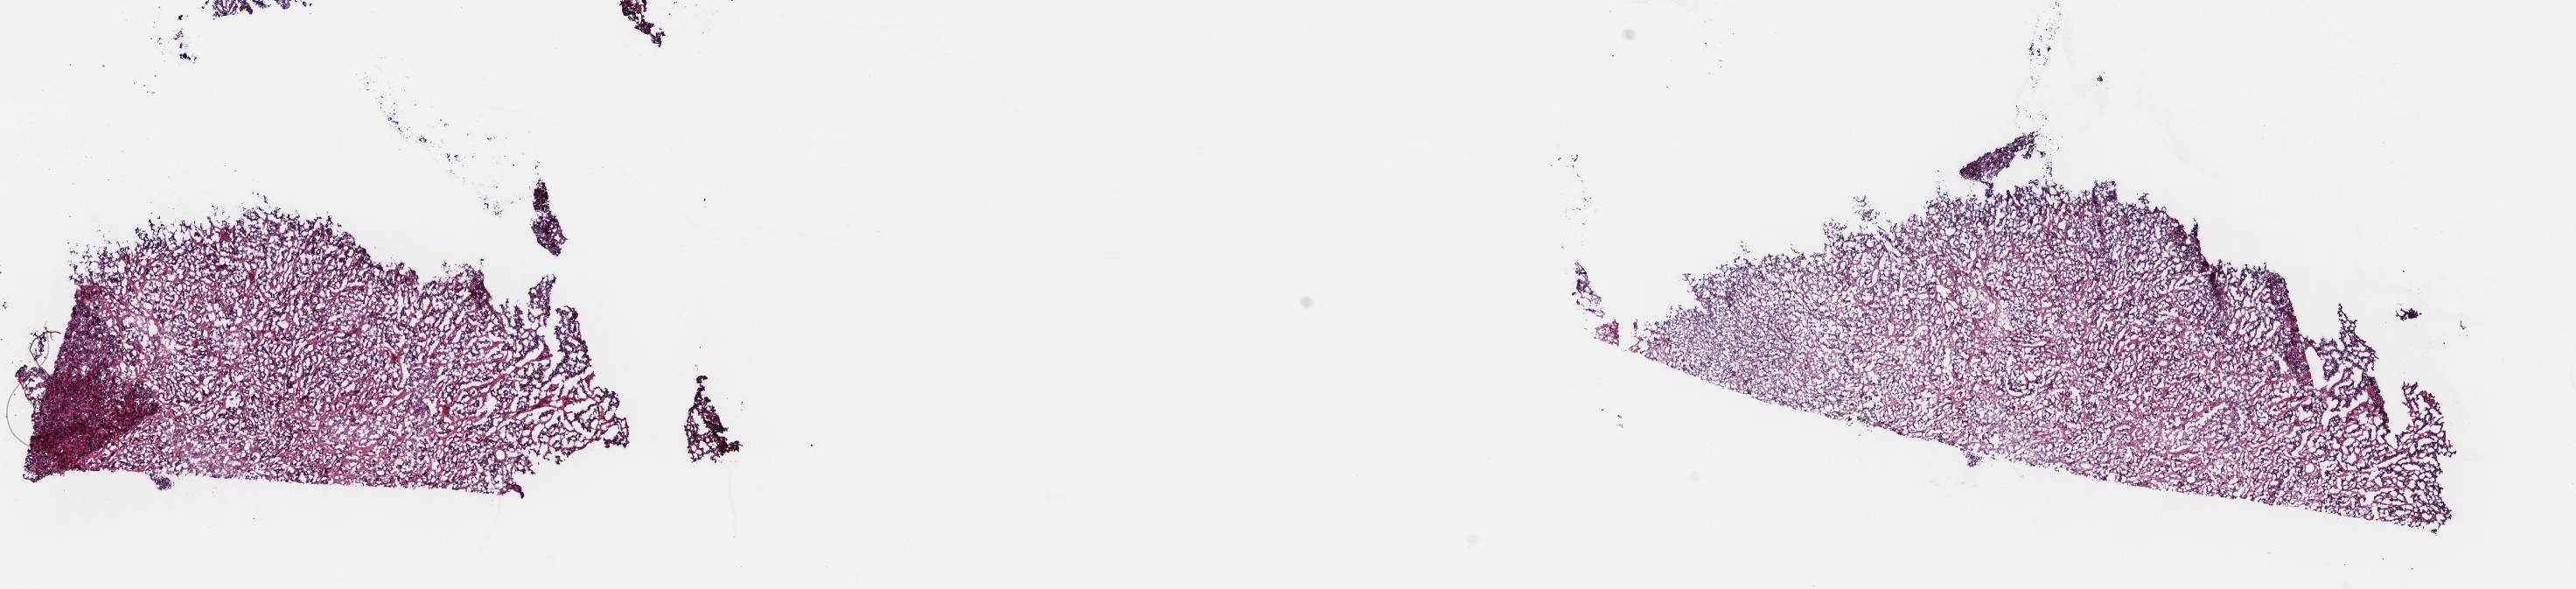
Whole-slide histology image, H&E — whole scanned area (about 23.1 x 5.3 mm, from a 40x scan) shown as a low-resolution overview. Frozen section. Primary tumour sample from the bladder. Patient: male, age at initial diagnosis 45 years. Histologic grade: high grade. Slide review estimates, as recorded: tumour cells 80%, tumour nuclei 80%, normal cells 0%, stromal cells 20%, necrosis 0%. Inflammatory infiltration, as recorded: lymphocyte infiltration 3%, monocyte infiltration 0%, neutrophil infiltration 0%.
AJCC pathologic stage: IV (6th edition). Pathologic diagnosis: Transitional cell carcinoma (anterior wall of bladder). Lymph nodes positive (case pathology): 2 of 41 examined.